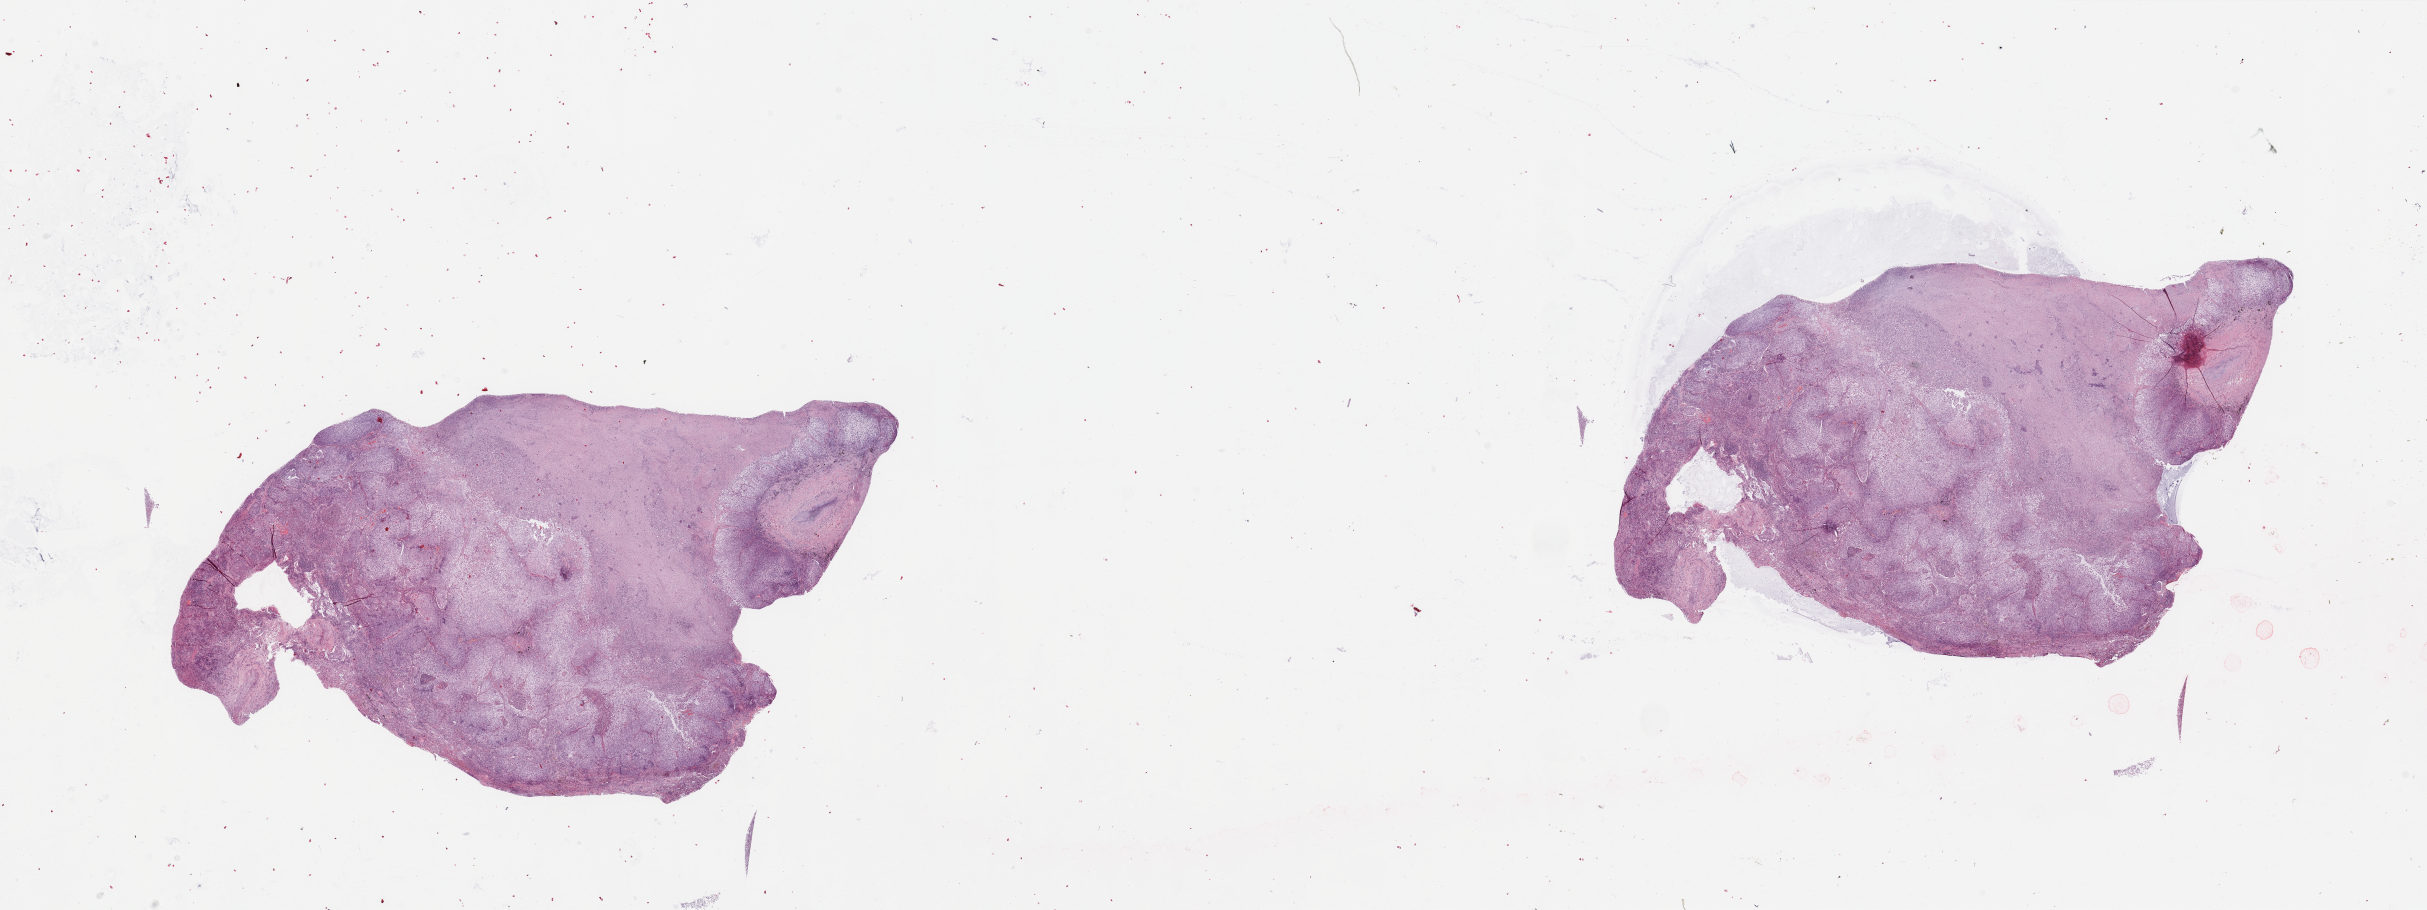
Whole-slide histology image, Hematoxylin and eosin (H&E) stained — whole scanned area (about 38.4 x 14.4 mm) shown as a low-resolution overview. Tumour tissue sample, lung. 53-year-old male patient. Histologic grade: G2 (moderately differentiated).
AJCC pathologic stage: IIIA. Histologic diagnosis: Squamous cell carcinoma, NOS.